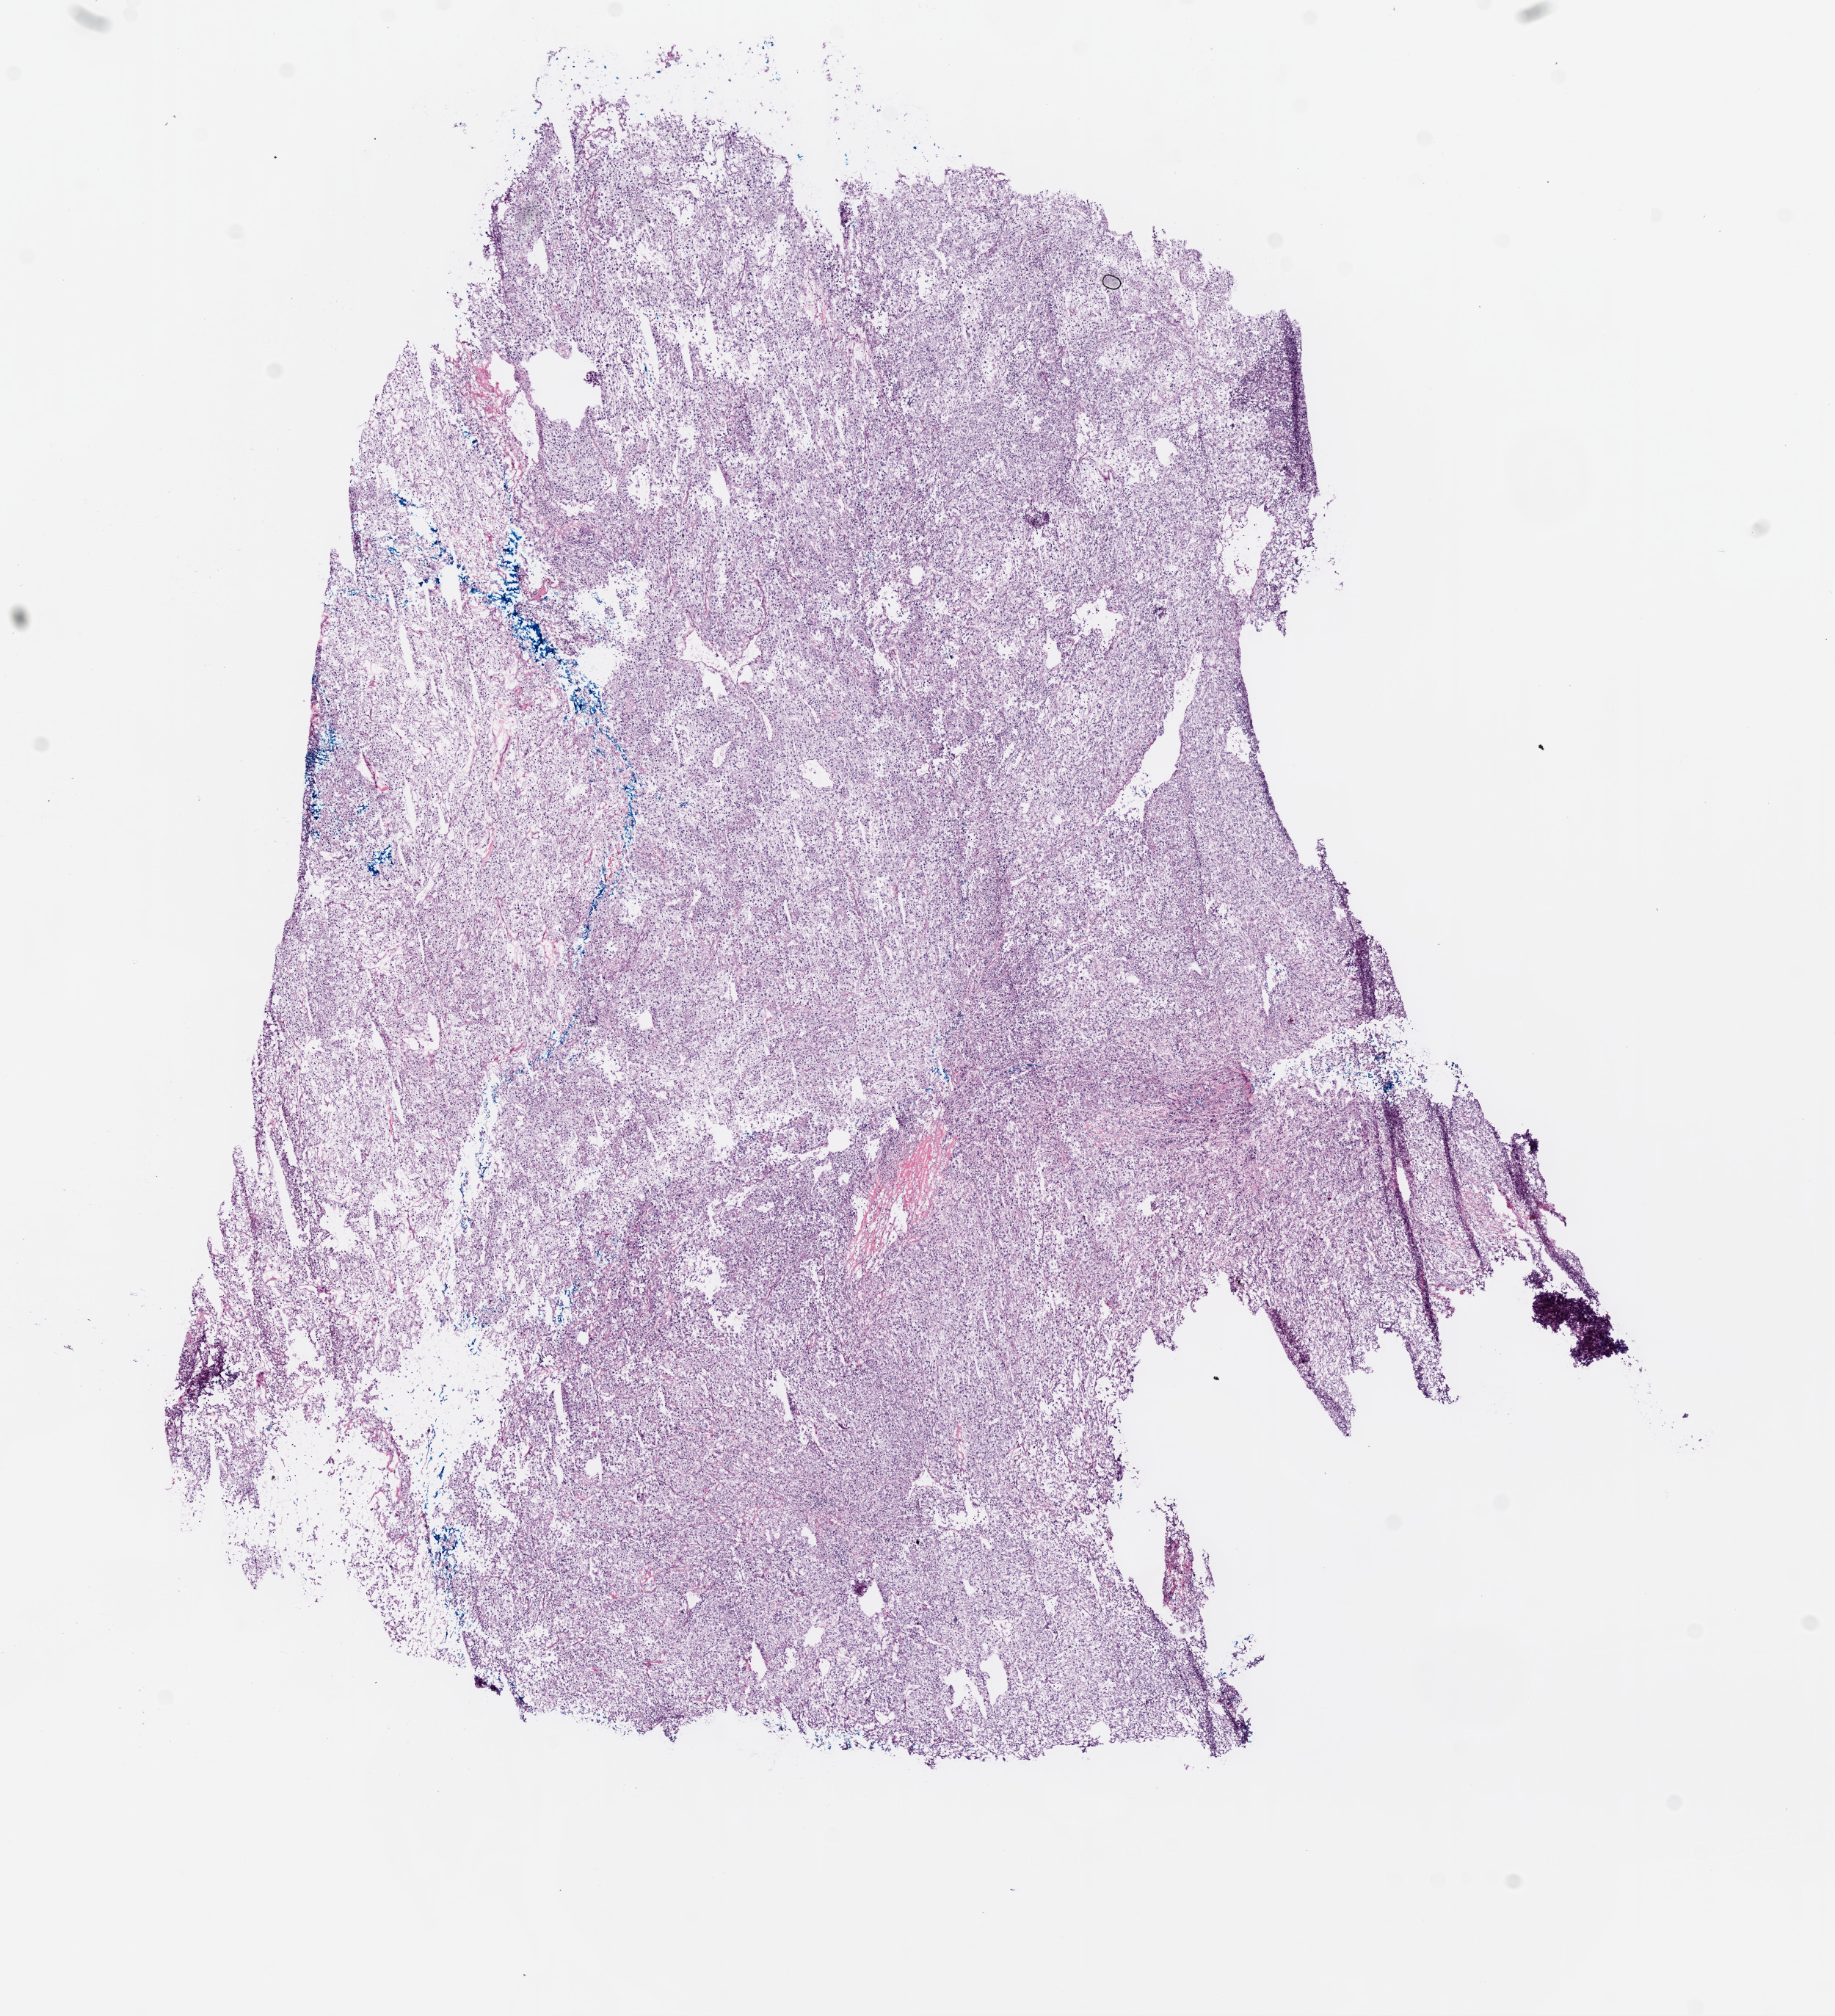
H&E-stained whole-slide image — low-resolution overview of the scanned area, about 10.0 x 11.0 mm. Frozen section from the bottom of the tissue portion. Primary tumour sample from the kidney. Female patient; age at initial diagnosis 75 years. Histologic grade: G4 (undifferentiated). Slide review estimates, as recorded: tumour cells 95%, tumour nuclei 80%, normal cells 0%, stromal cells 5%, necrosis 0%.
AJCC pathologic stage: I. Laterality: right. Pathologic diagnosis: Clear cell adenocarcinoma, NOS.